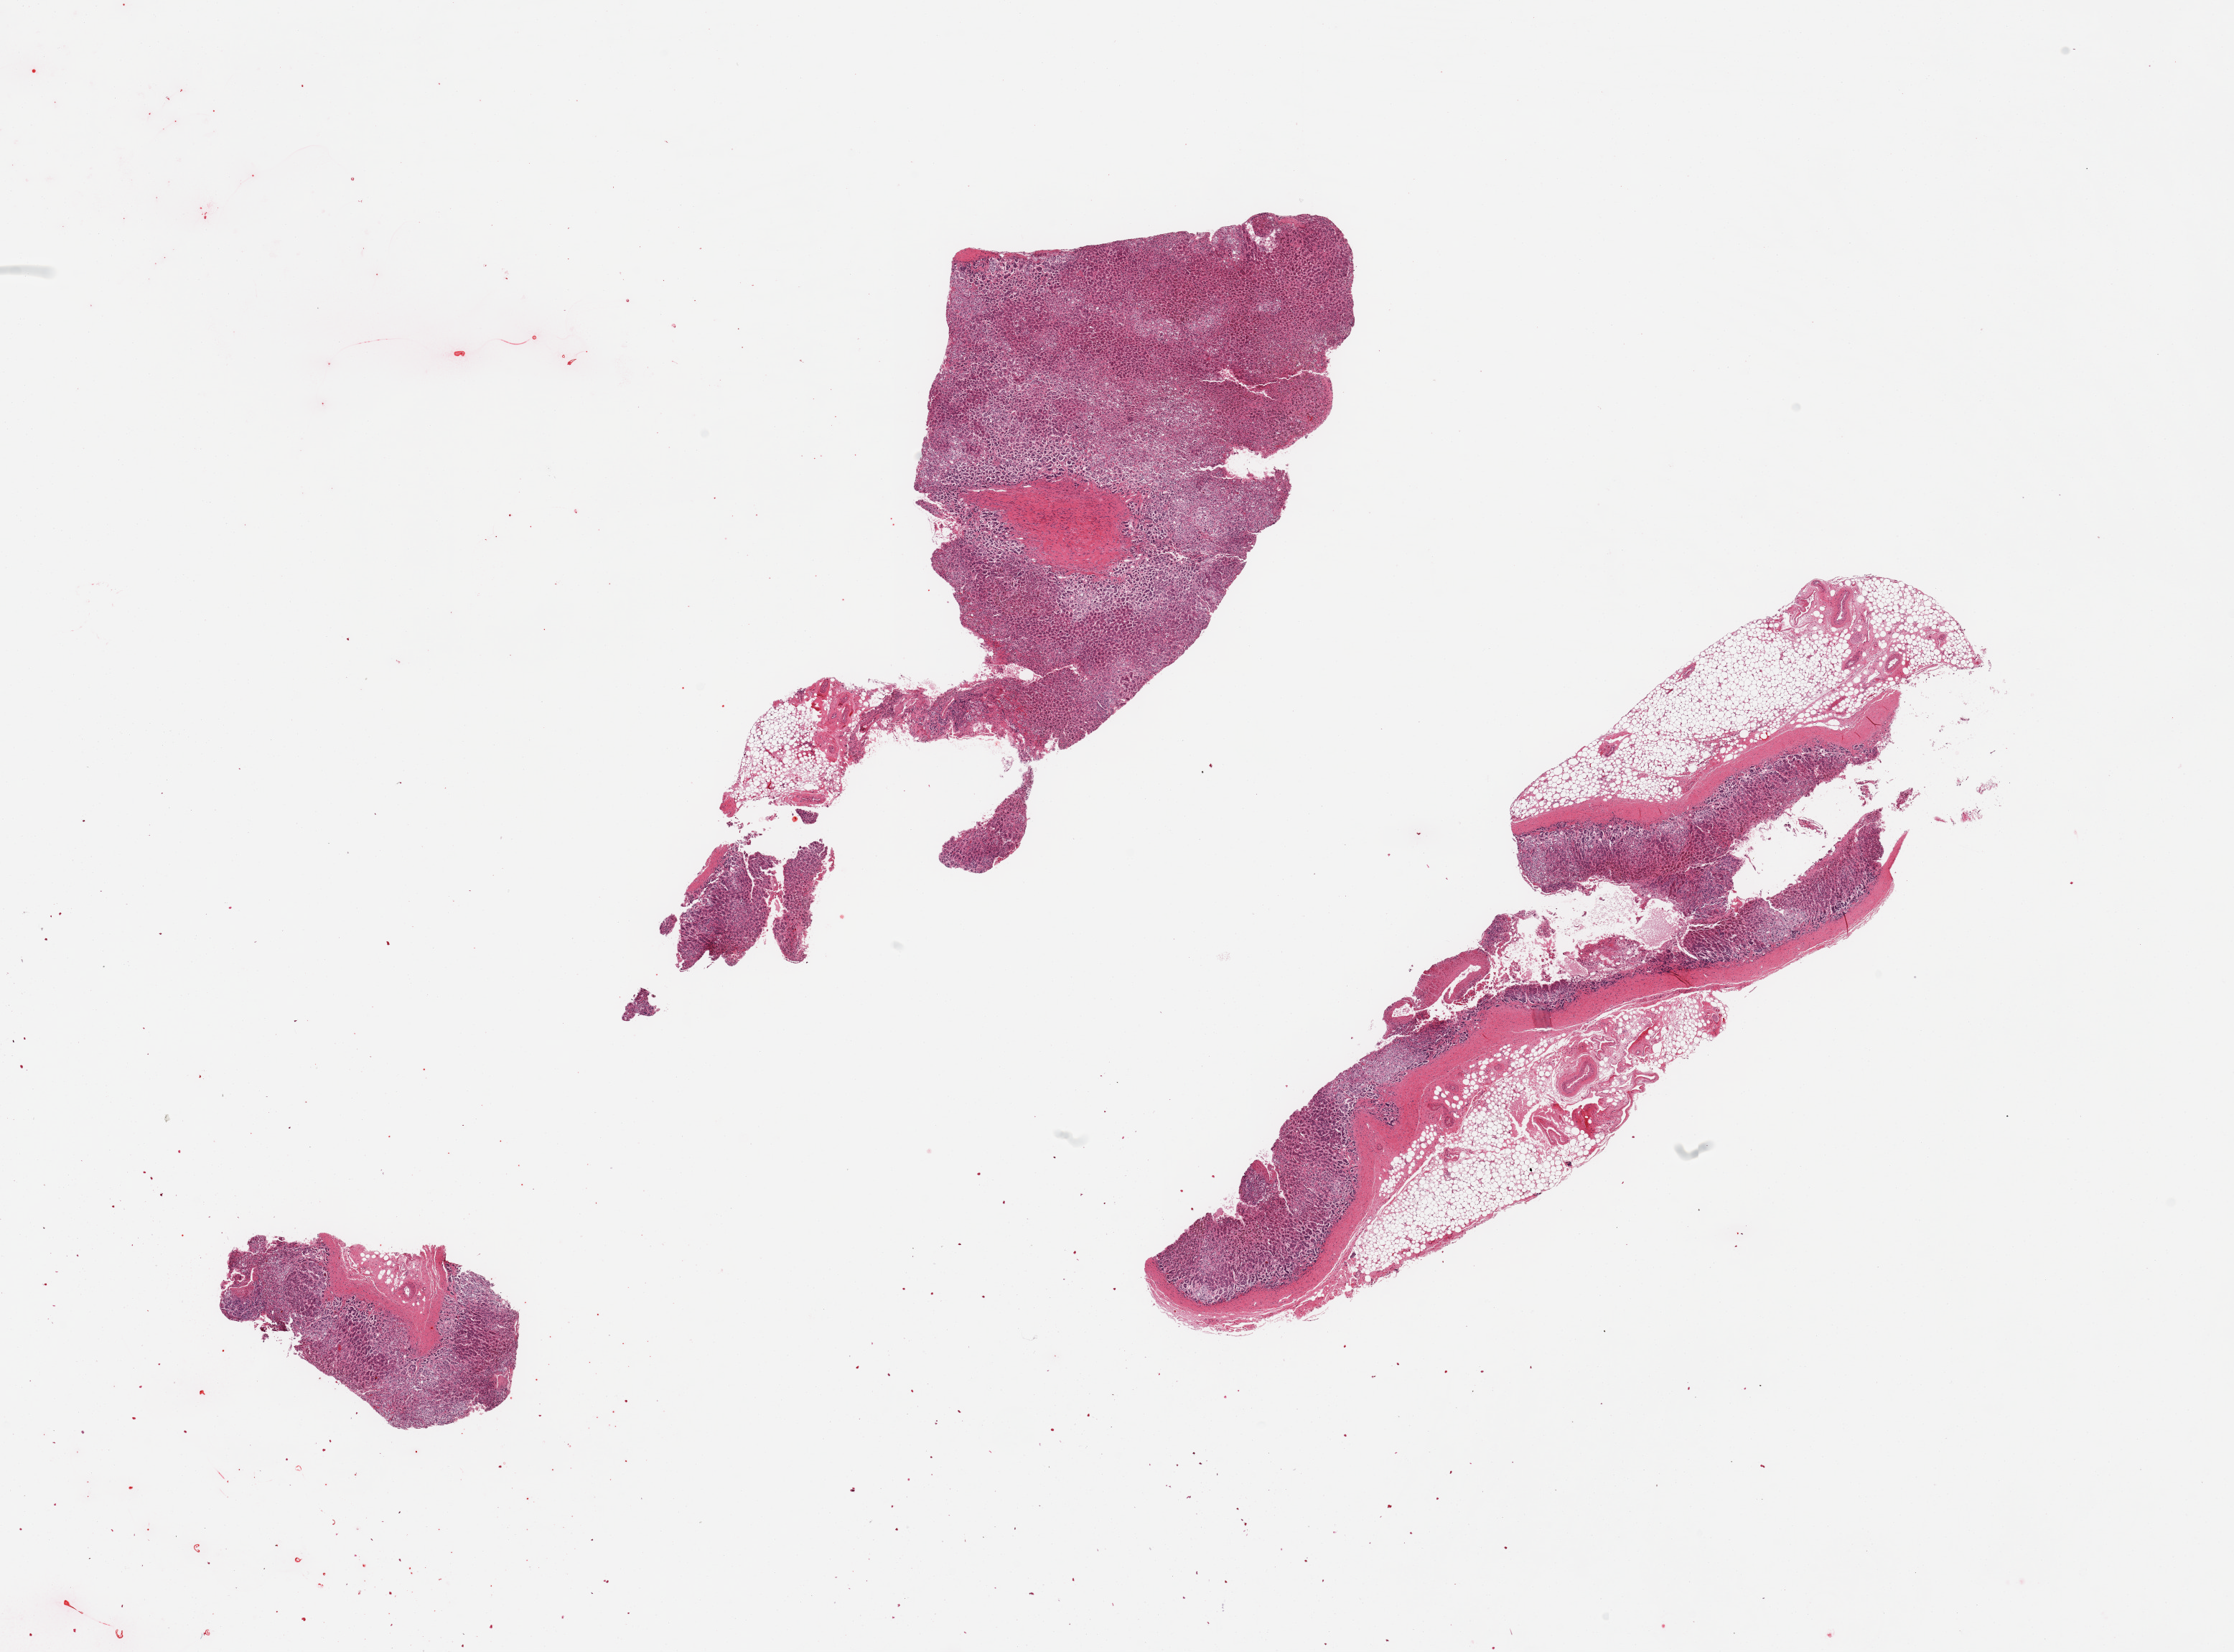
Digitized haematoxylin and eosin-stained section — whole scanned area (about 24.6 x 18.2 mm) shown as a low-resolution overview, PAXgene-fixed, paraffin-embedded tissue, target tissue: adrenal gland, tissue donor sample. Female donor.
Pathologist's review note for this sample: 2 fragmented pieces: 1 with 60% fat.